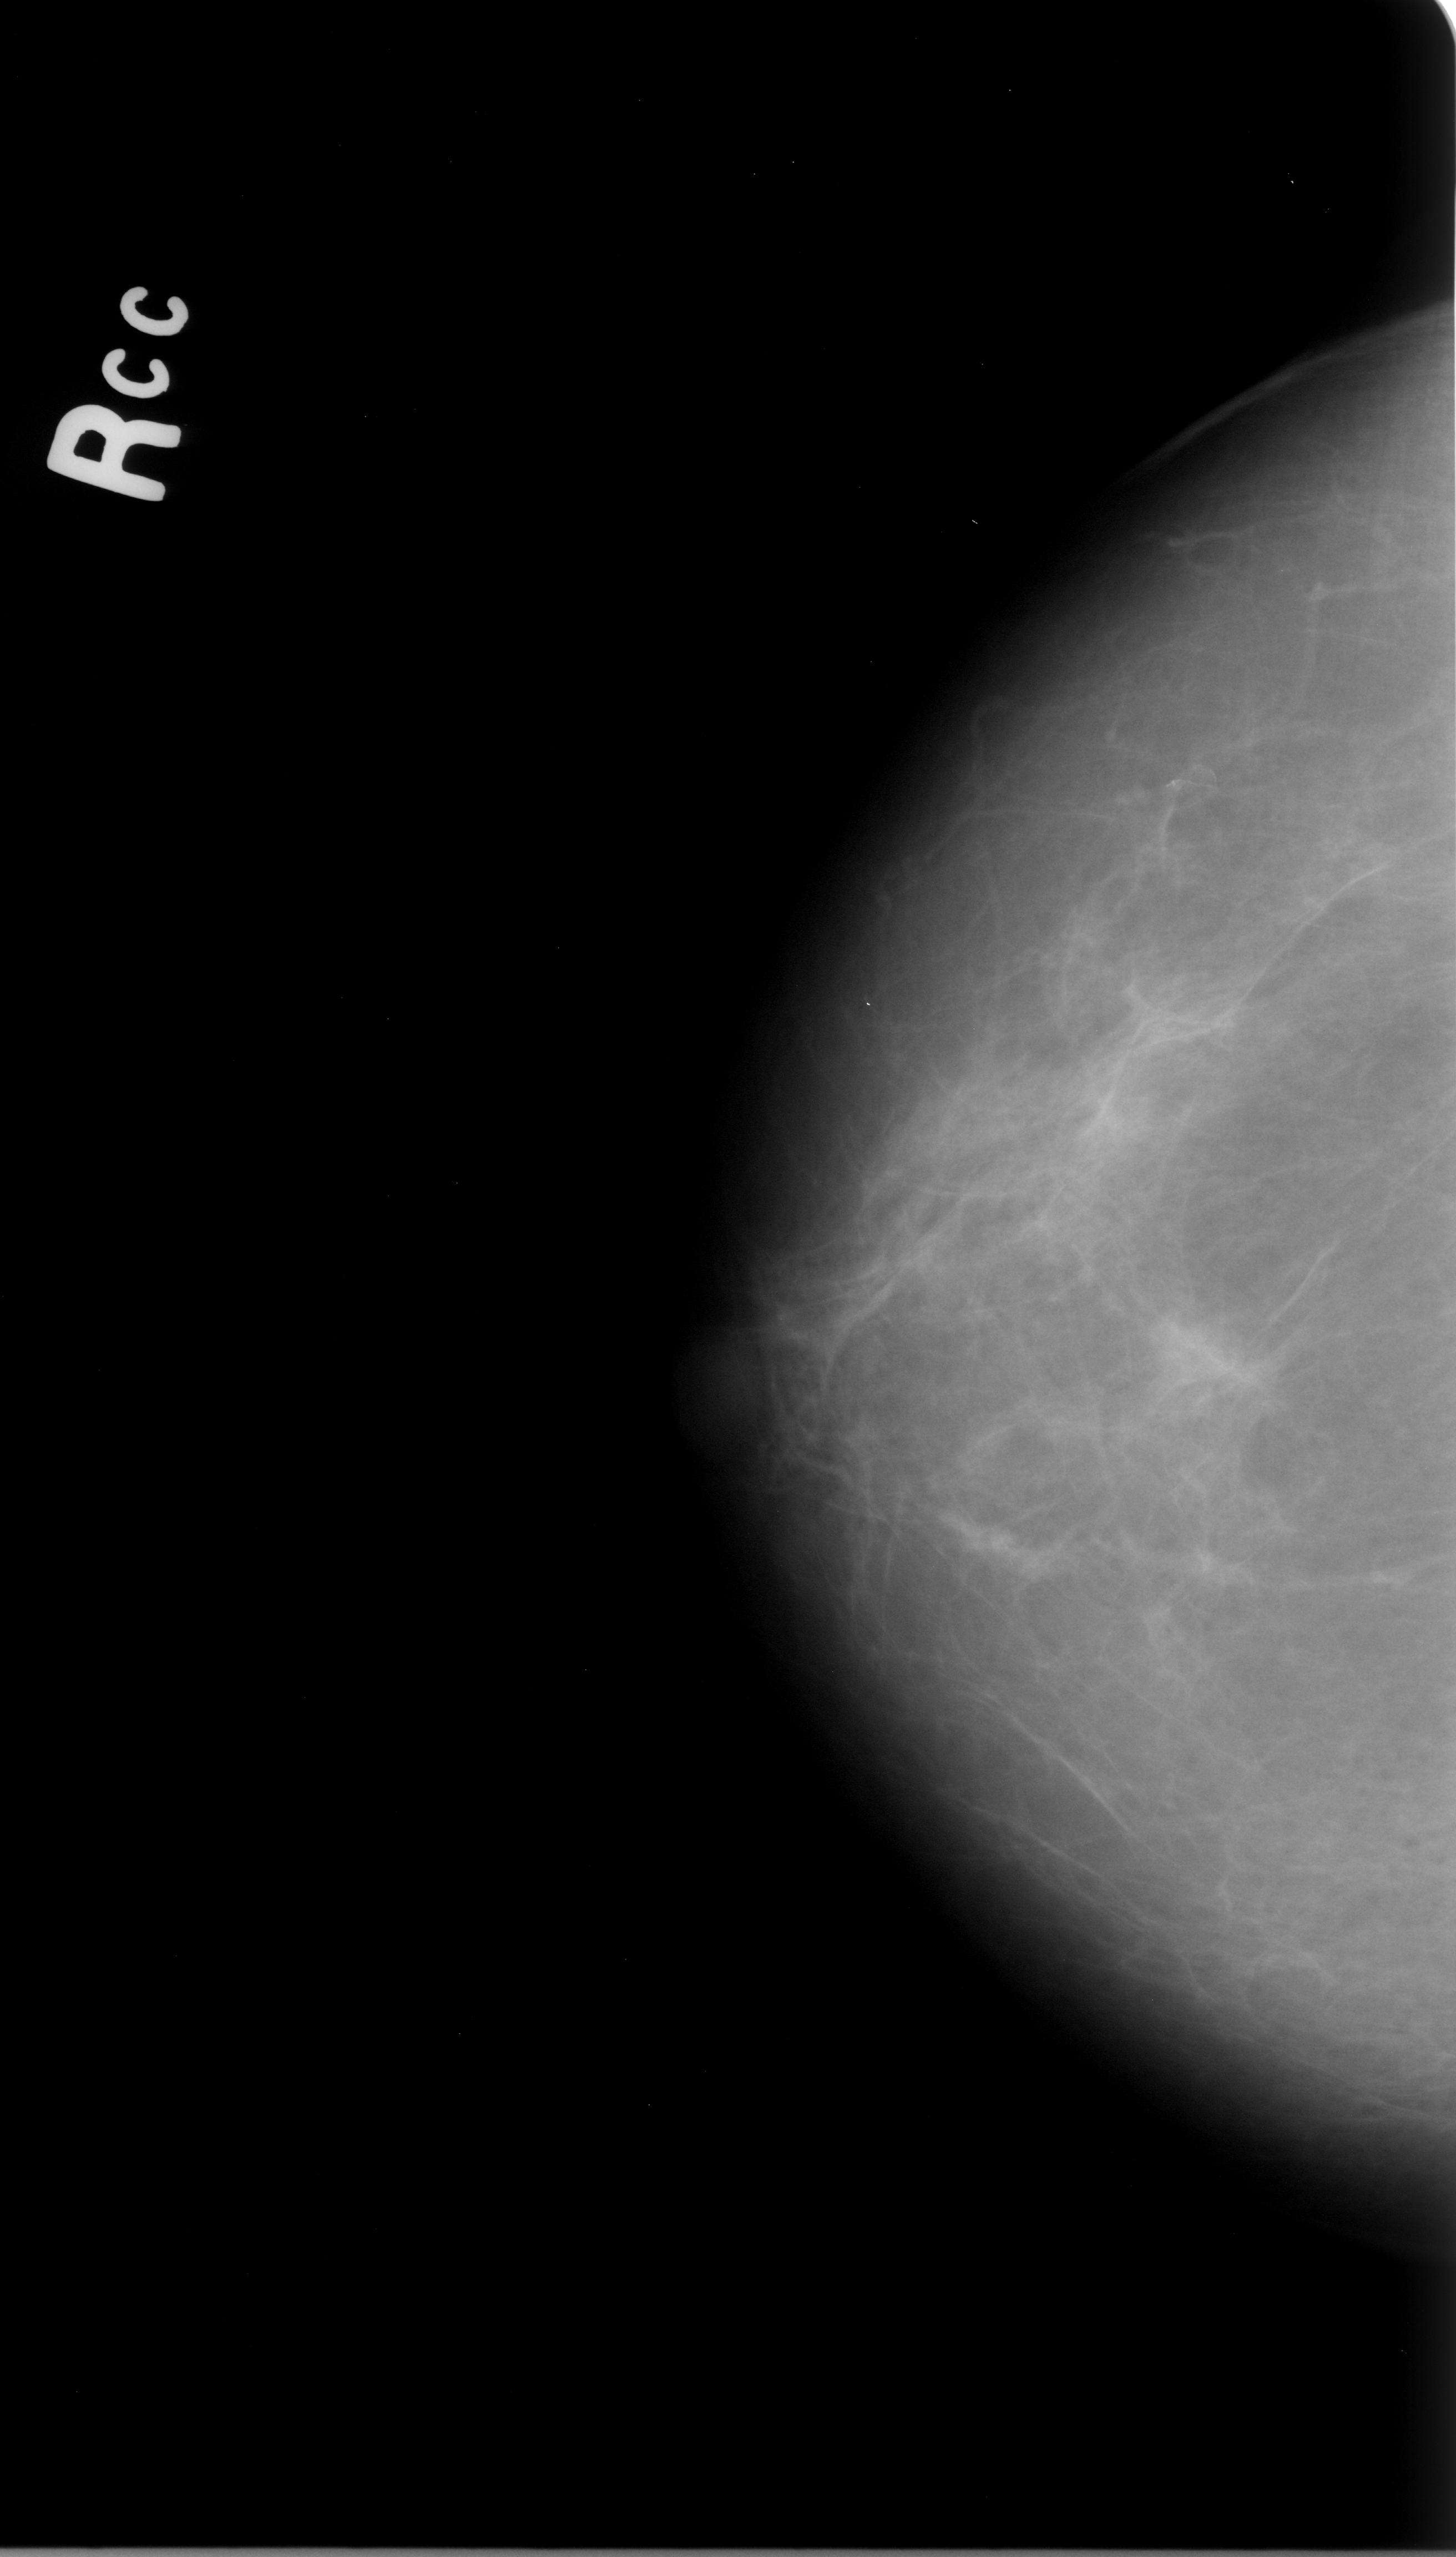
Digitized screen-film mammogram, right breast, CC view, BI-RADS breast density category 1 (scale 1–4).
- Marked findings (only marked abnormalities are described; nothing is implied about the rest of the image): mass, shape irregular, margins ill defined; BI-RADS assessment category 5; pathology result (as recorded, not read from the image): malignant.